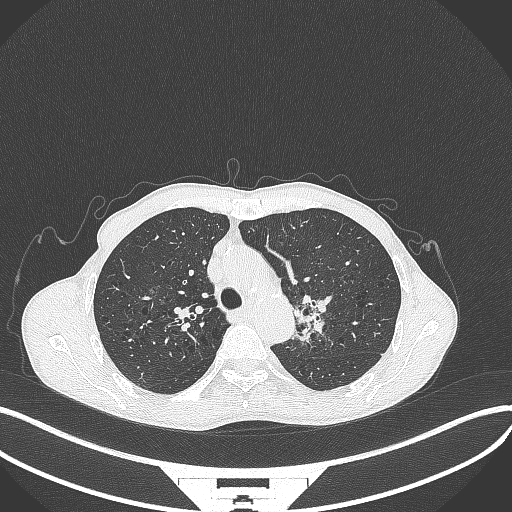
Chest CT, one axial slice. Position 304 of 386 along the scan axis. 120 kVp. Lung window (W 1500 / L -600 HU). 512 × 512 image matrix, field of view 400 × 400 mm. Male patient, age 65 years. From the clinical record (not read from this slice): clinical TNM (as recorded): T2b N0 M0; histopathological grade: G2.
Outlined on this slice (bounding box drawn by a radiologist):
- lung tumour (recorded histology: adenocarcinoma): bounding box (x1, y1, x2, y2) in pixels: (290, 290, 330, 342)